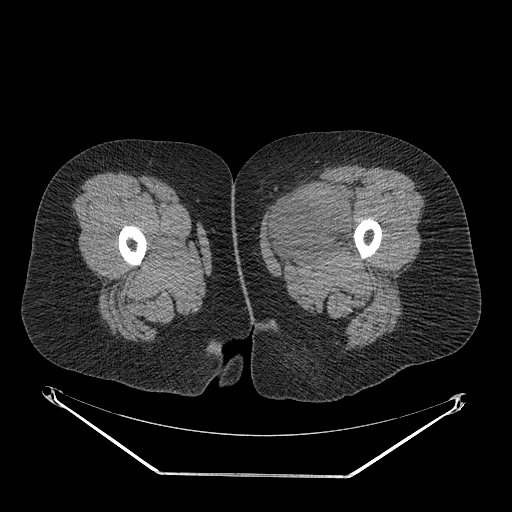
CT of an extremity soft-tissue mass (from a PET/CT study), one axial slice. Position 23 of 267 along the scan axis. Soft-tissue window (W 400 / L 40 HU). 3.75 mm slice thickness. 512 × 512 image matrix, field of view 500 × 500 mm. Female patient. From the clinical record (not read from this slice): histological type: myxofibrosarcoma; grade: intermediate; site of the primary tumour: left thigh.
Annotated regions visible in this slice (expert contour drawn on MRI and transferred to this co-registered scan by the dataset authors):
- gross tumour volume including surrounding oedema: bounding box <269,185,355,259> (left, top, right, bottom; pixels)
- gross tumour volume (mass): <270,189,353,254>